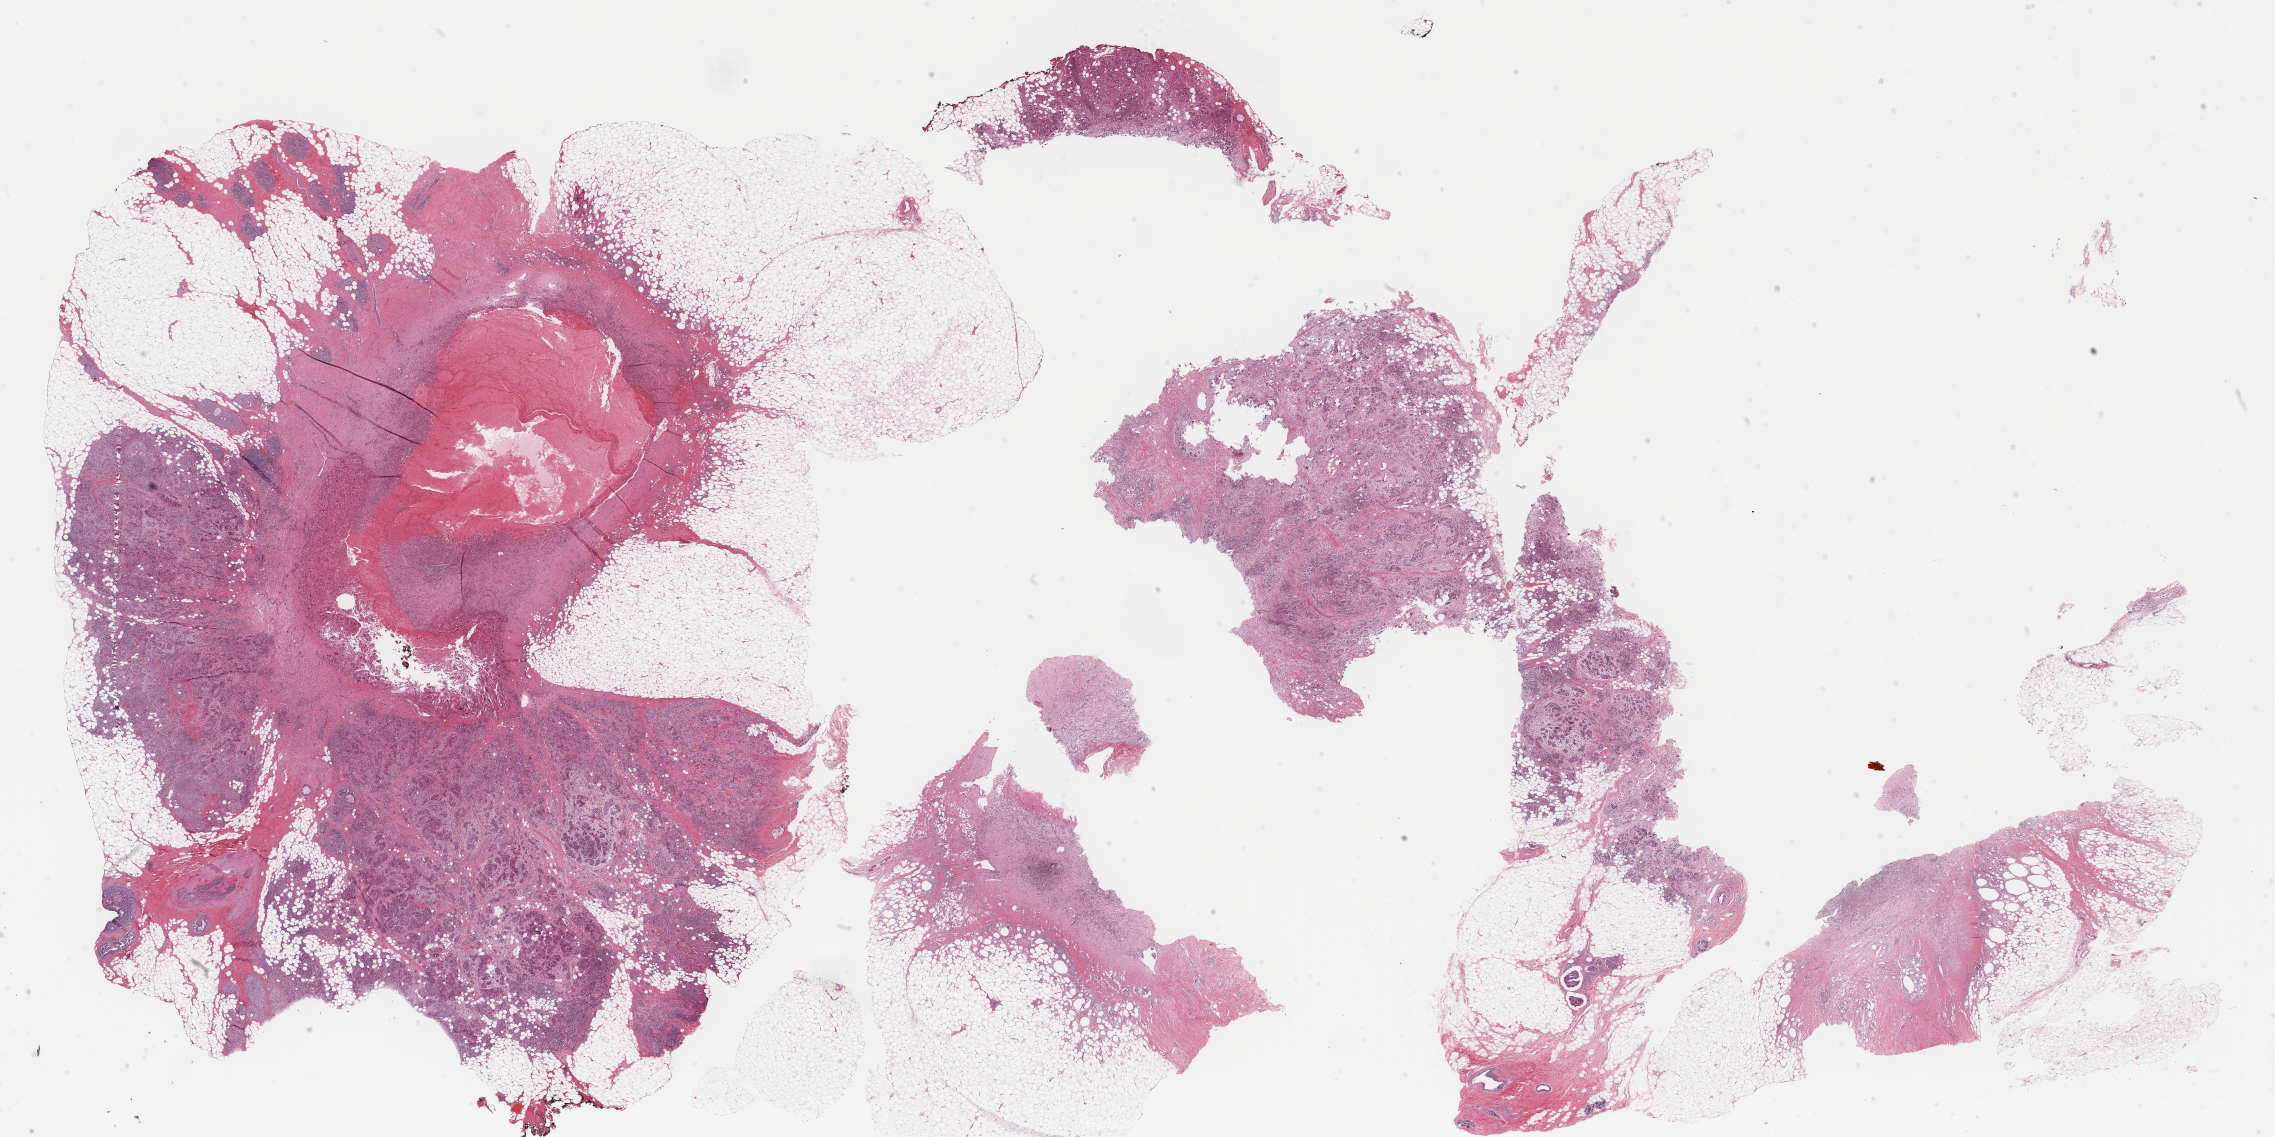
H&E whole-slide image, low-resolution overview of the scanned area, about 36.1 x 18.1 mm (acquisition: 40x scan), FFPE section, primary tumour sample from the breast. Female, age 50 years at initial diagnosis.
TNM: T1 N0 M0. Lymph nodes positive (case pathology): 0 of 4 examined. AJCC pathologic stage: I. Histologic diagnosis: Infiltrating duct carcinoma, NOS.